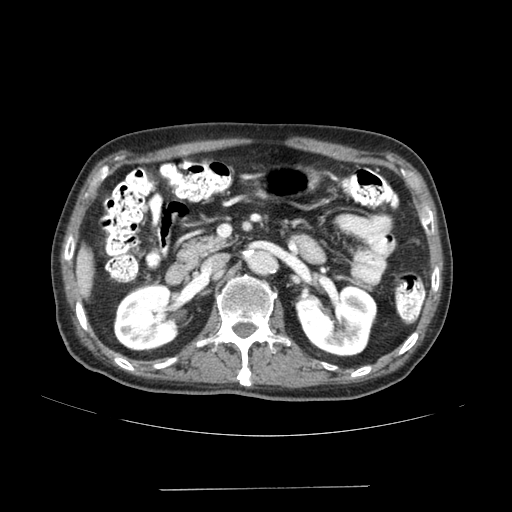
Contrast-enhanced abdominal CT (liver protocol), one axial slice. Slice 58 of 192 in the series (ordered by position). Soft-tissue window (W 400 / L 40 HU). 2.5 mm slice thickness. 512 × 512 image matrix, field of view 400 × 400 mm. From the clinical record (not read from this slice): diagnosis: hepatocellular carcinoma (patient treated with transarterial chemoembolisation; whether this scan precedes or follows treatment is not stated here); TNM stage (as recorded): Stage-IVA; Child-Pugh class: A; tumour differentiation: poorly differentiated.
Outlined on this slice (semi-automatic segmentation, software-assisted and operator-edited):
- liver parenchyma outside the tumour (the mass and vessels are separate outlines, so this box may not span the whole liver): bounding box <76,246,93,296> (left, top, right, bottom; pixels)